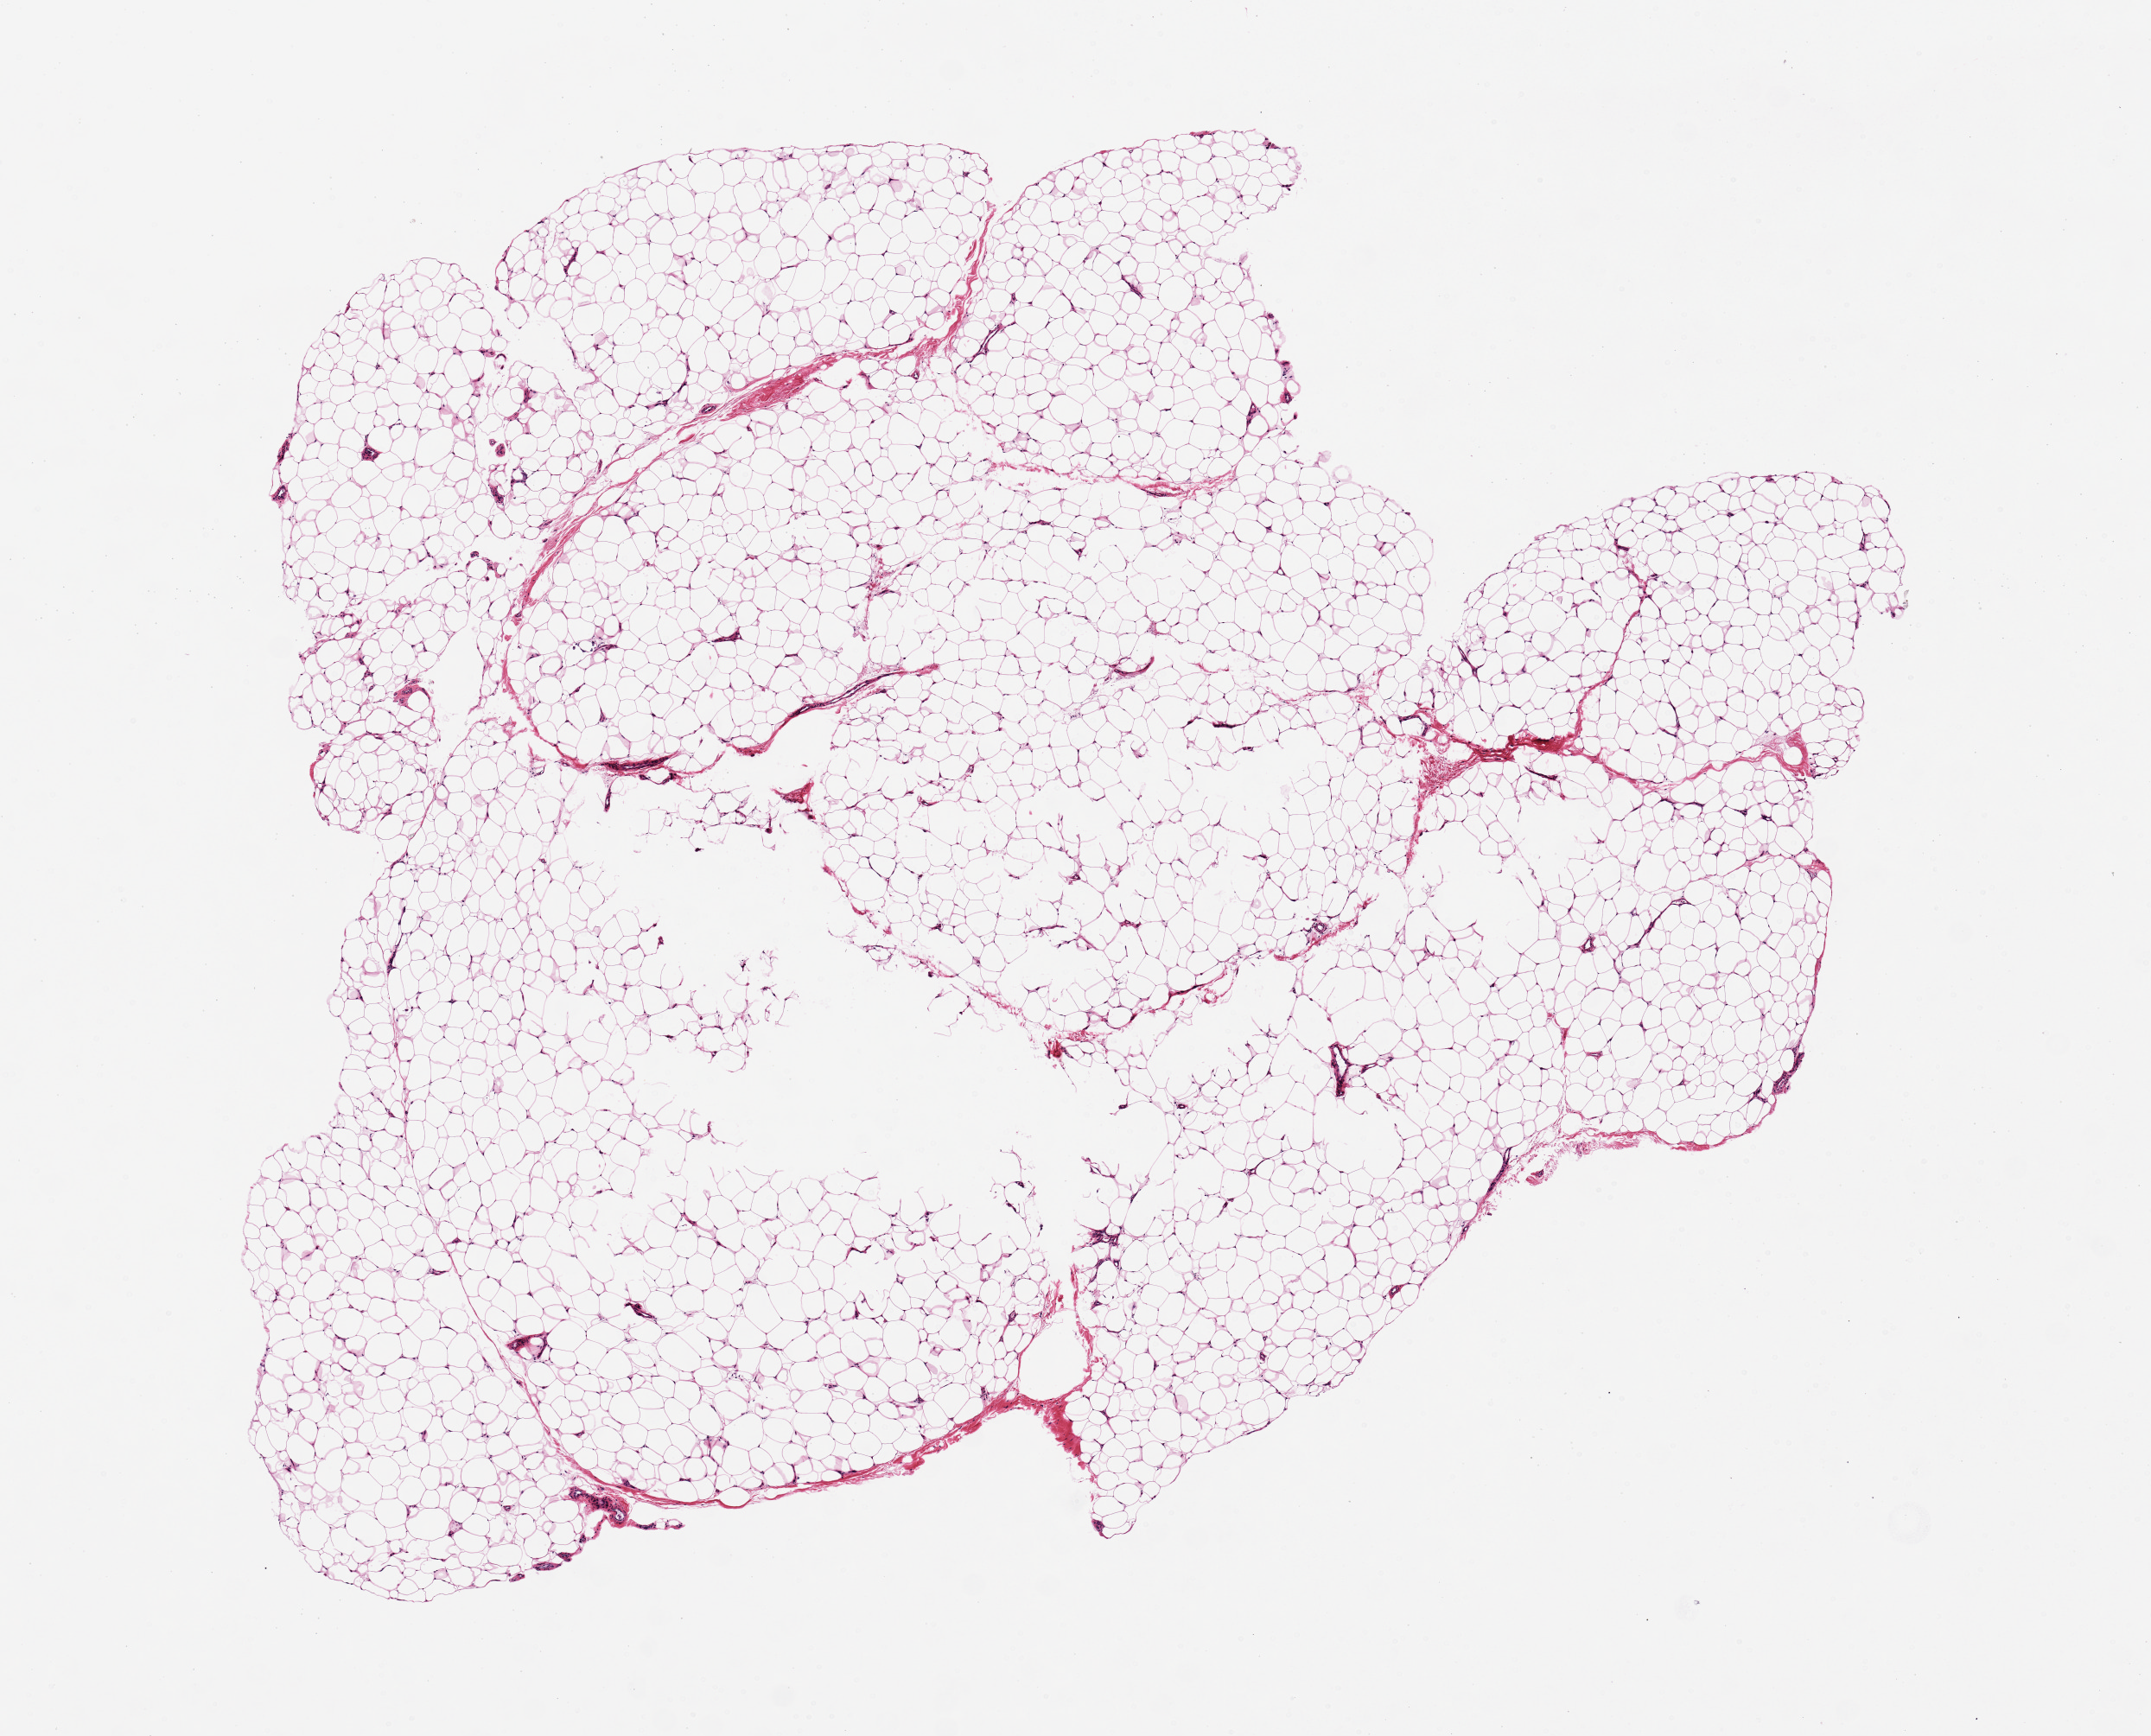
Hematoxylin and eosin (H&E) whole-slide image, brightfield — a low-resolution overview of the entire scanned area, about 9.8 x 7.9 mm, PAXgene-fixed, paraffin-embedded tissue, target tissue: adipose tissue, donor tissue sample.
* review note (as recorded): About 8% unfixed centrally. 8.5x6.5mm